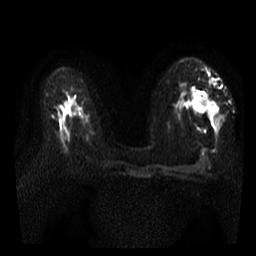
Breast MRI, one axial slice; position 19 of 35 along the scan axis; diffusion-weighted series; image 2 of 4 stored at this slice position (different b-values; order by instance number); 3 T; 256 × 256 image matrix, field of view 300 × 300 mm. Female patient.
Outlined on this slice (manually delineated by an expert):
- tumour on diffusion-weighted imaging: bounding box <194,95,216,114> (left, top, right, bottom; pixels)